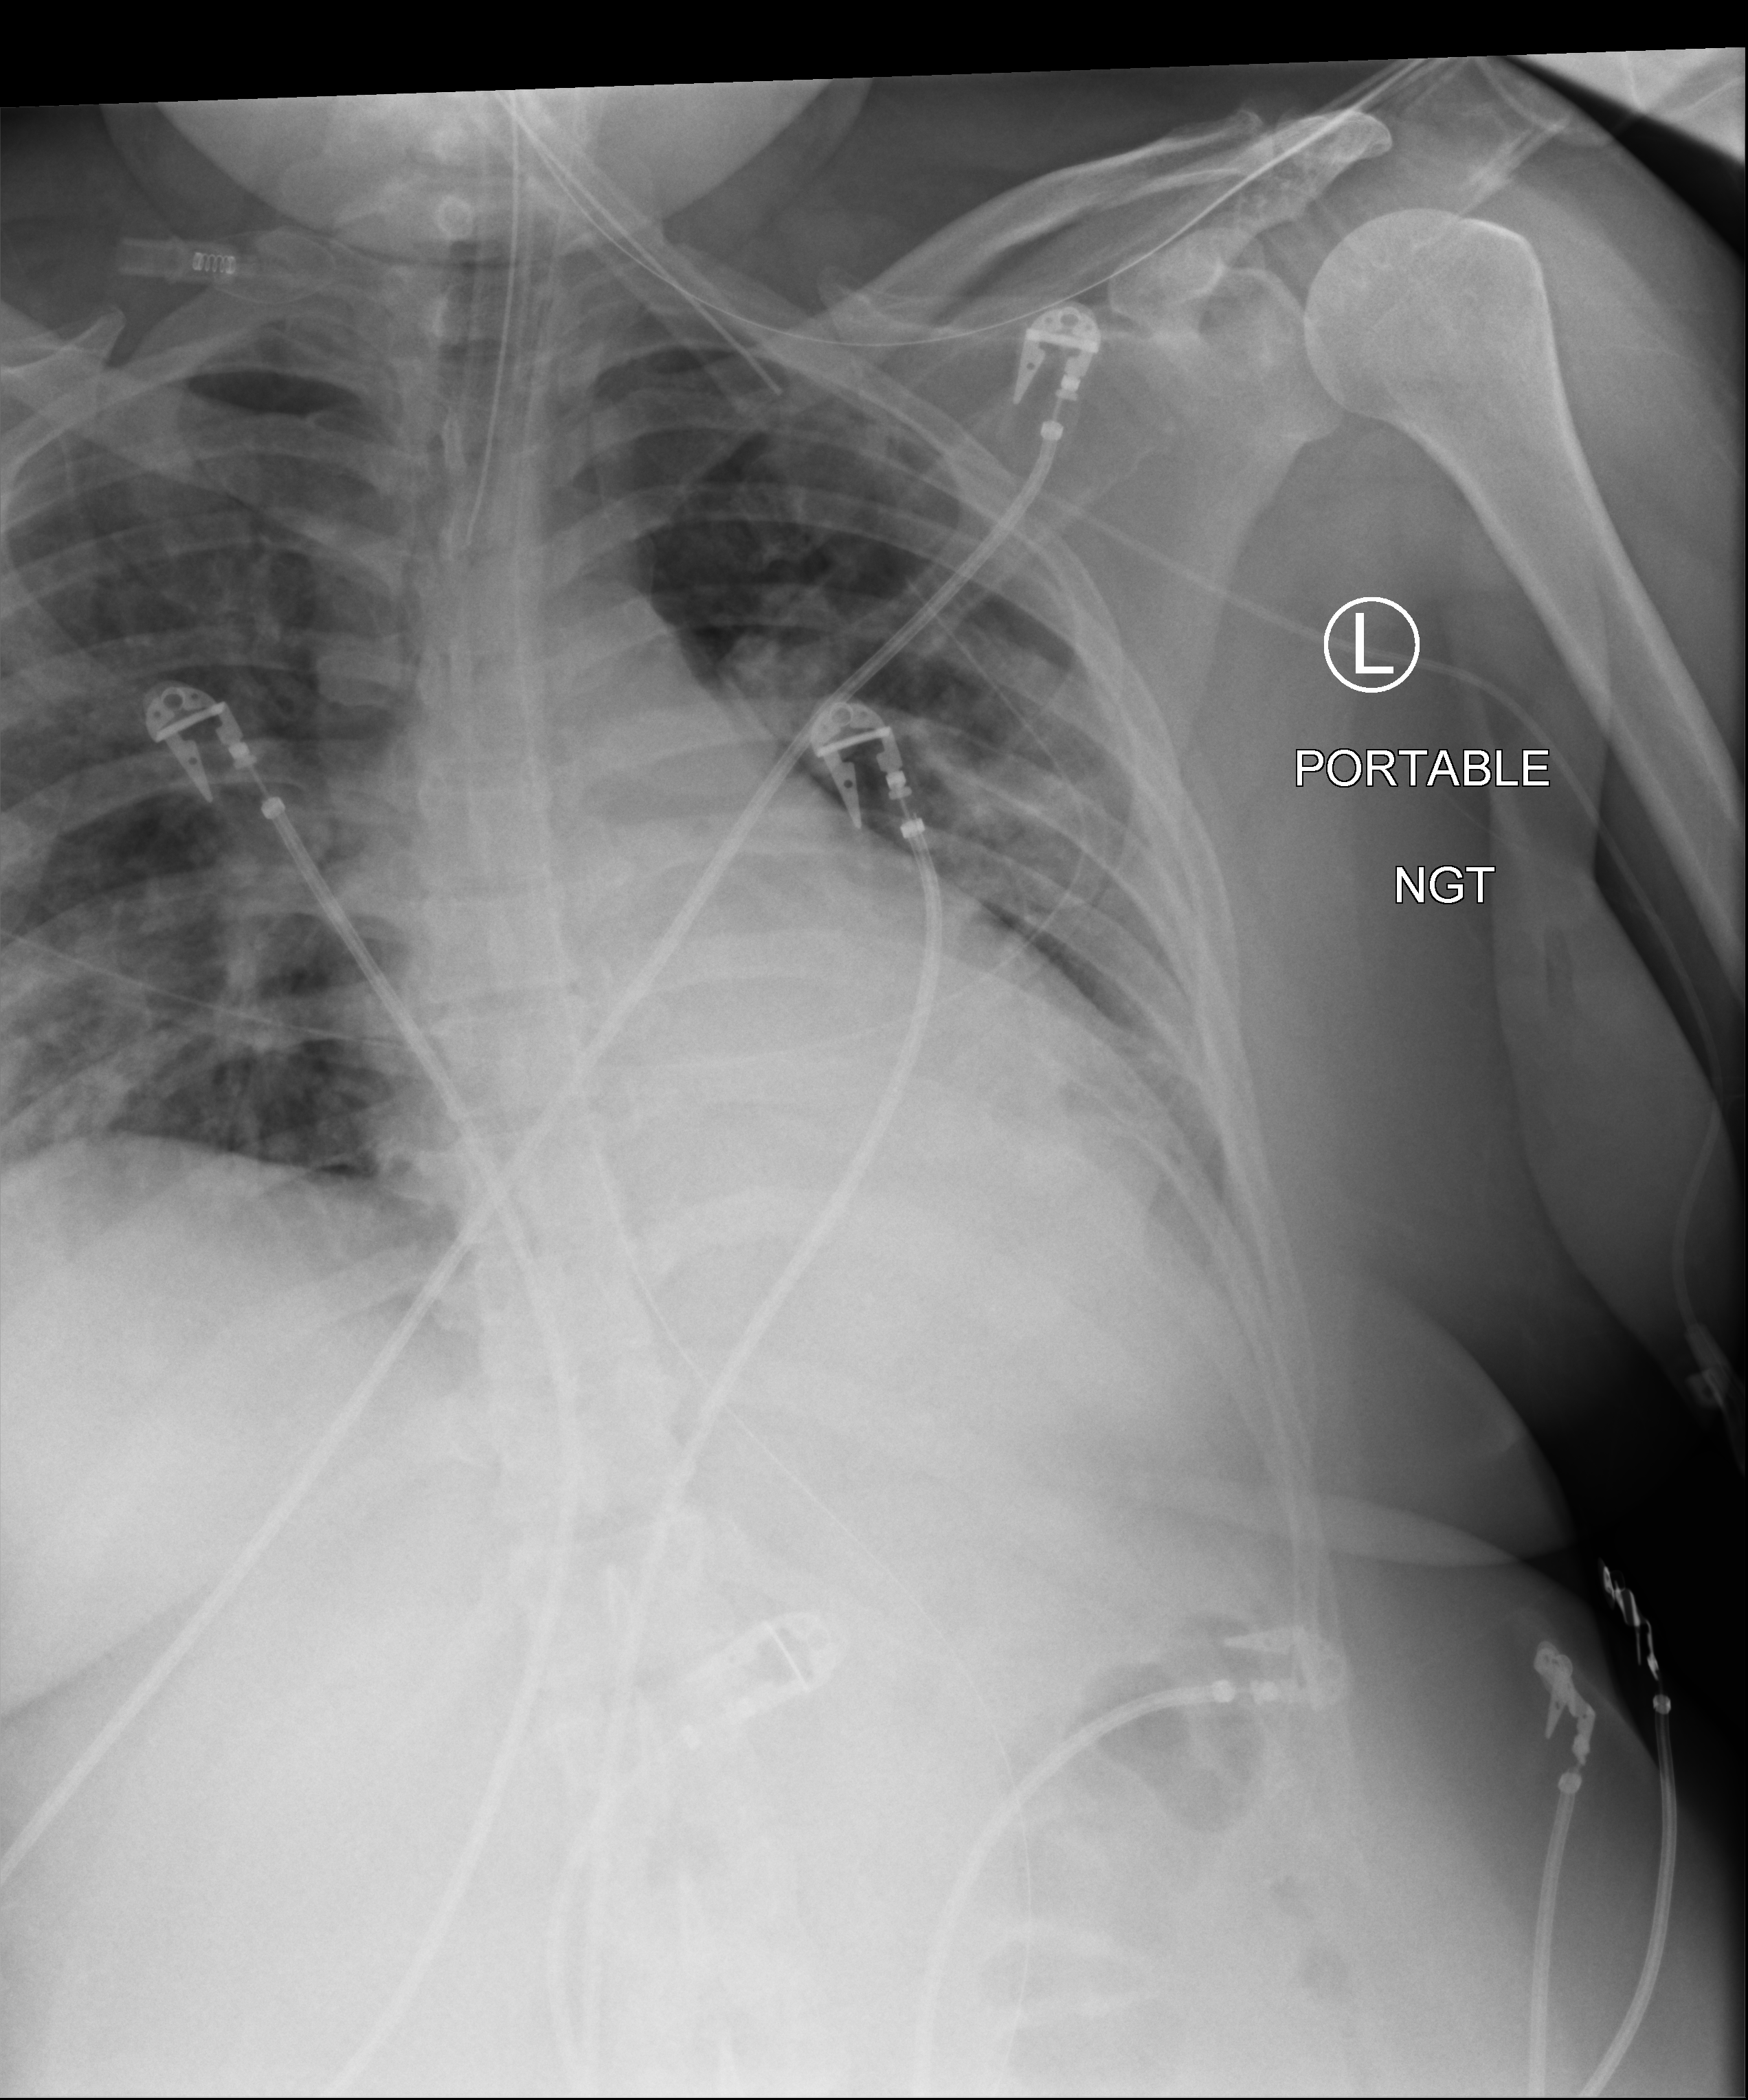
Chest X-ray (portable); anteroposterior (AP) projection. Patient hospitalised with COVID-19; female, aged 18–59 years.
Admission-level facts for this patient (not findings on this image; timing relative to this image not recorded):
- mechanically ventilated during this hospital stay: yes
- smoking status (admission record): never
- length of hospital stay: 16 days